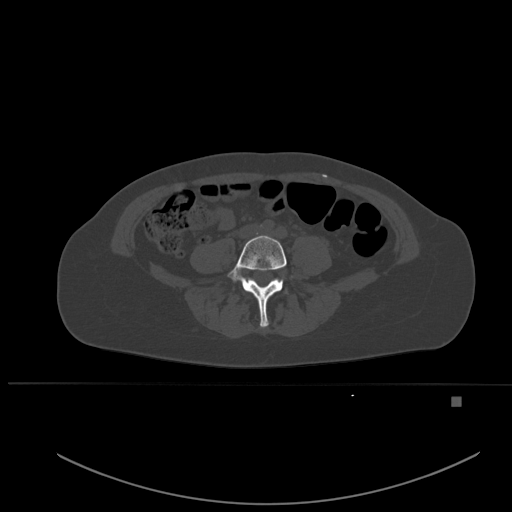
CT including the spine, one axial slice. Slice 171 of 651 in the series (ordered by position). Bone window (W 1800 / L 400 HU). 1.5 mm slice thickness. 512 × 512 image matrix, field of view 443 × 443 mm. Patient: female, 49 years. Case-level facts recorded for this patient, not image findings: primary cancer: breast; vertebrae with lytic lesions (as recorded): L3, T12, L4.
Annotated regions visible in this slice (semi-automatic segmentation, software-assisted and operator-edited):
- L4 vertebra: bounding box <227,235,287,328> (left, top, right, bottom; pixels)